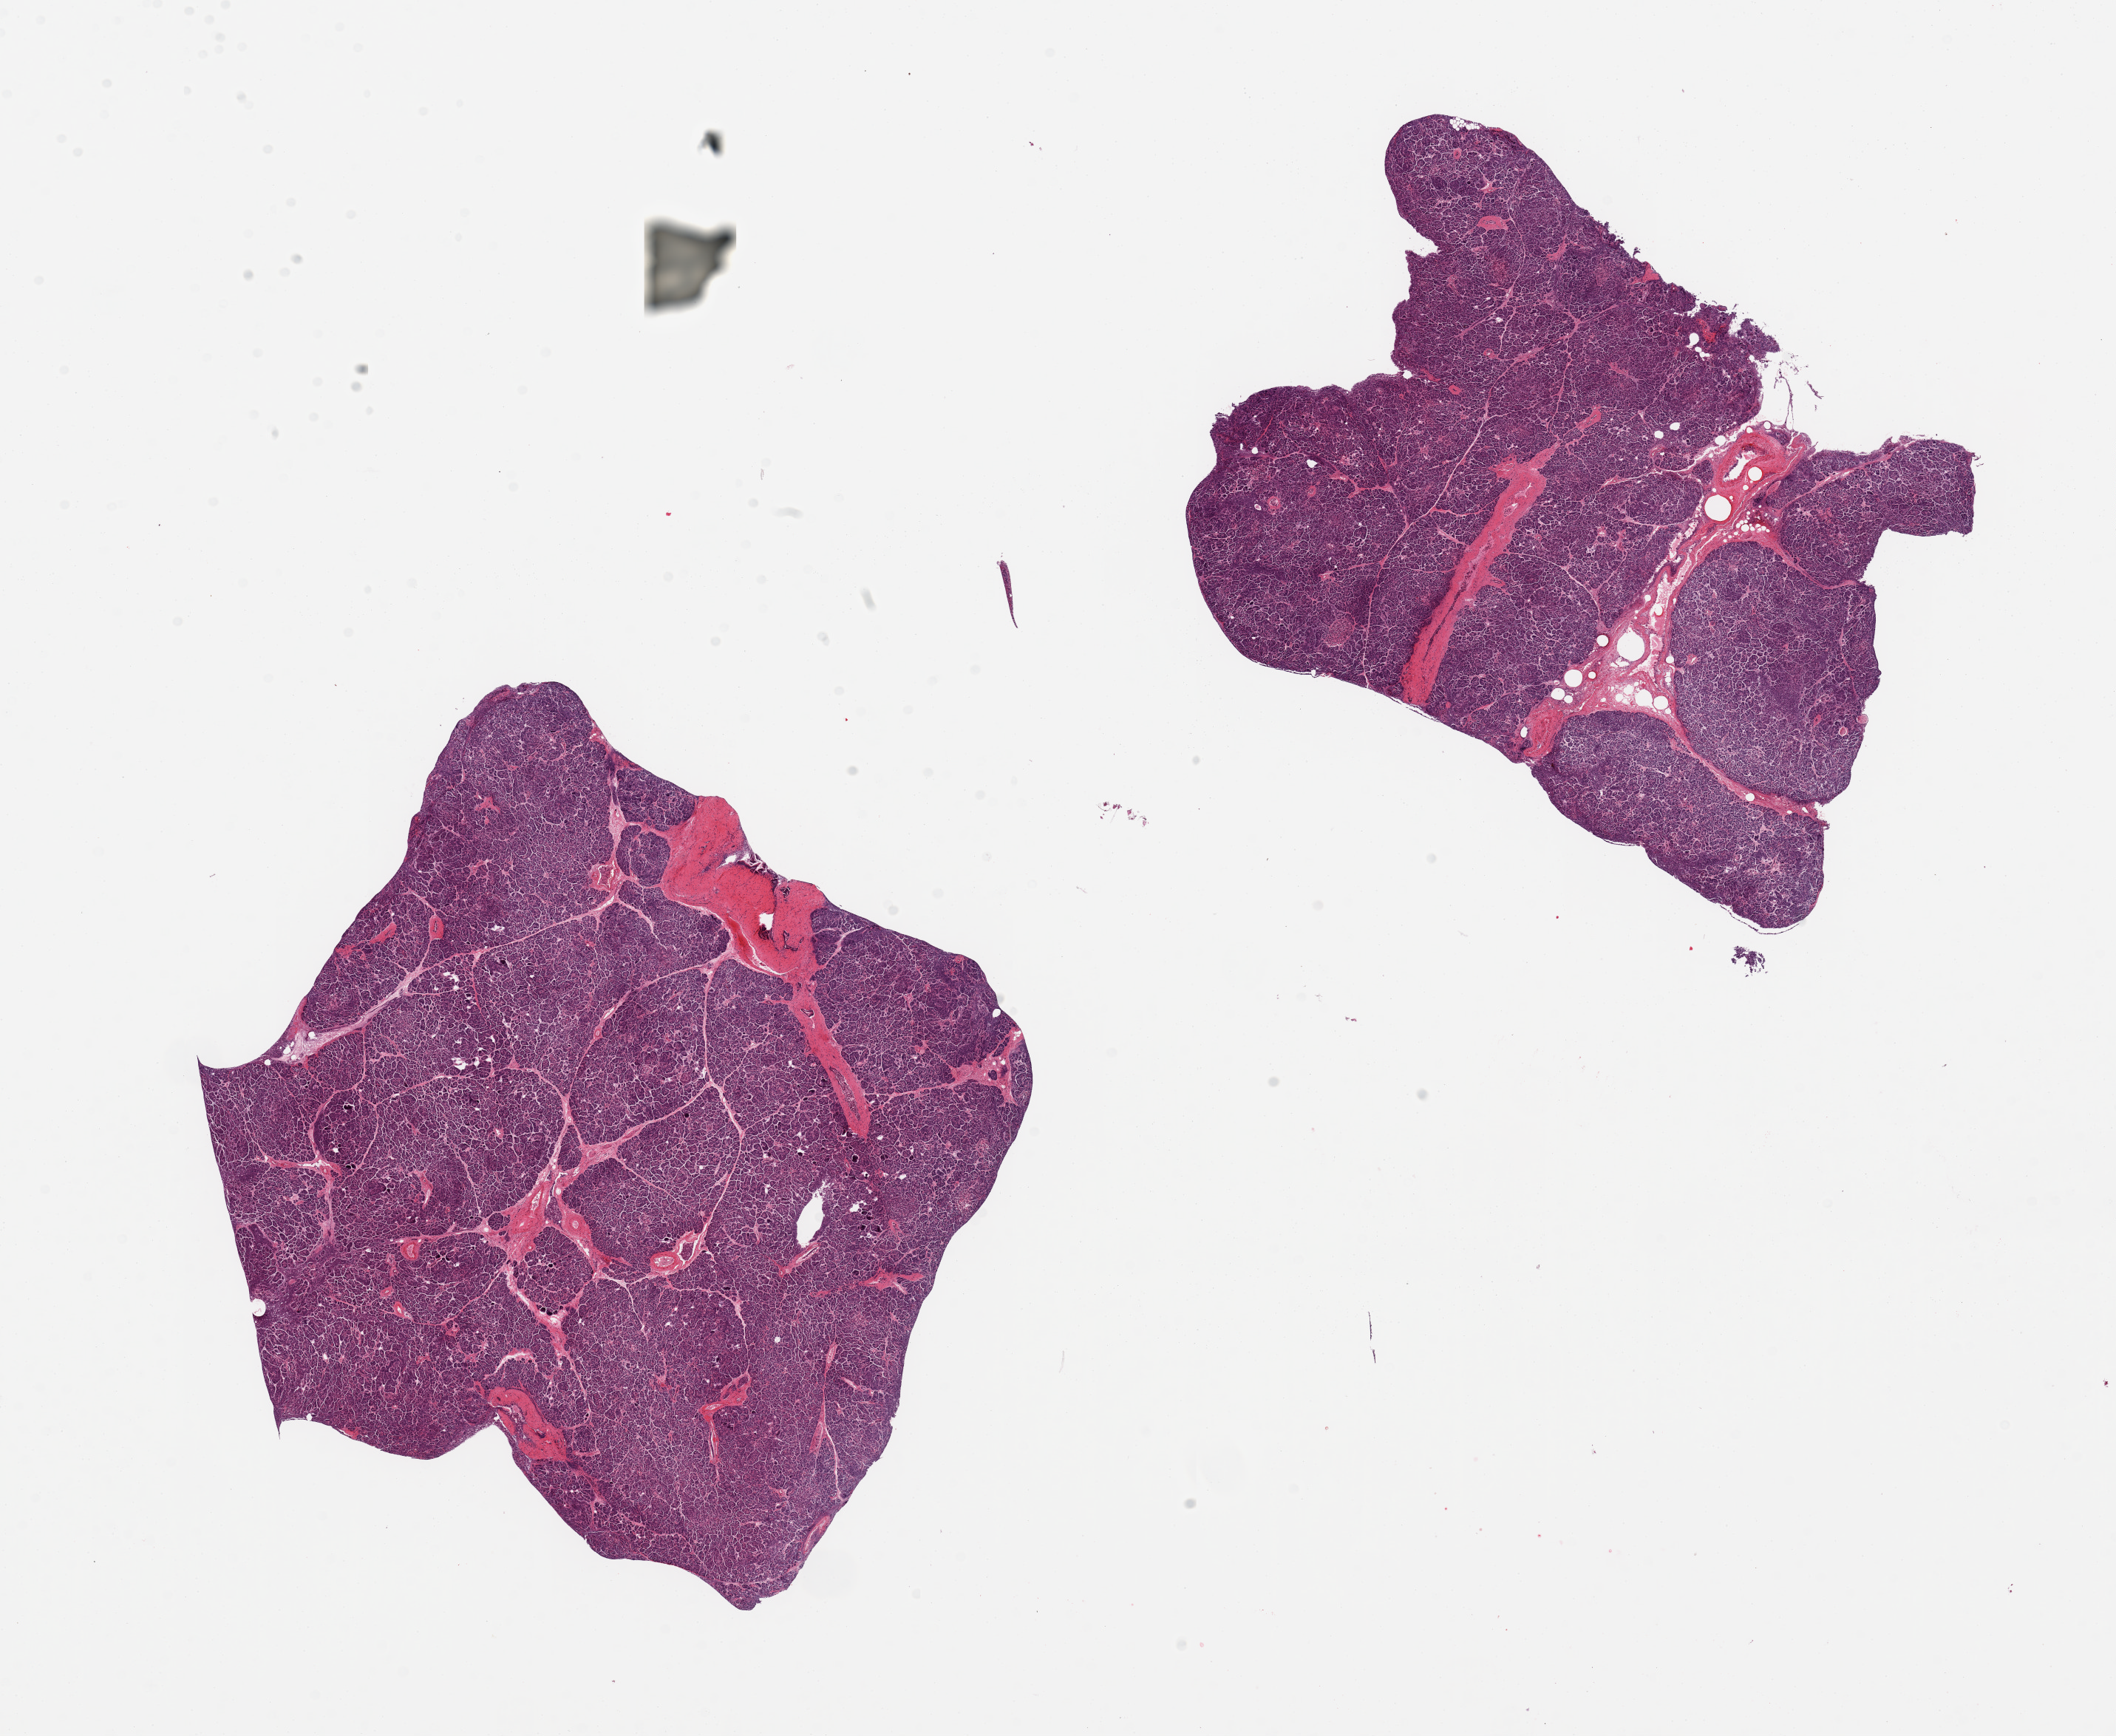
Digitized hematoxylin and eosin (H&E)-stained section — shown as a low-resolution overview of the whole scanned area (about 22.6 x 18.6 mm, acquisition: 20x scan); PAXgene-fixed, paraffin-embedded tissue; sampled site (target tissue): pancreas; tissue donor sample. Donor sex: male.
* pathologist's review note for this sample: 2 pieces; 1 with 10% internal fibroadipose and vascular tissue